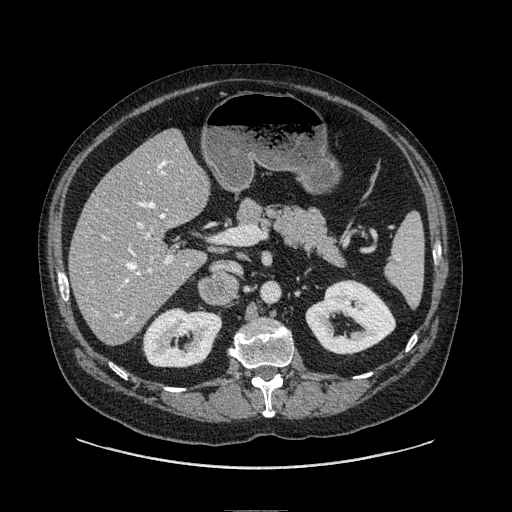
Contrast-enhanced abdominal CT, one axial slice; position 38 of 149 along the scan axis; soft-tissue window (W 400 / L 40 HU); 1.25 mm slice thickness; 512 × 512 image matrix, field of view 440 × 440 mm. Male patient. From the clinical record (not read from this slice): diagnosis: adrenocortical carcinoma; tumour side: right adrenal; tumour size at pathology: 7.5 cm; Ki-67 index: 15 %; stage (as recorded): 2.
Annotated regions visible in this slice (semi-automatically segmented with operator editing):
- mass: bounding box (x1, y1, x2, y2) in pixels: (200, 273, 237, 303)